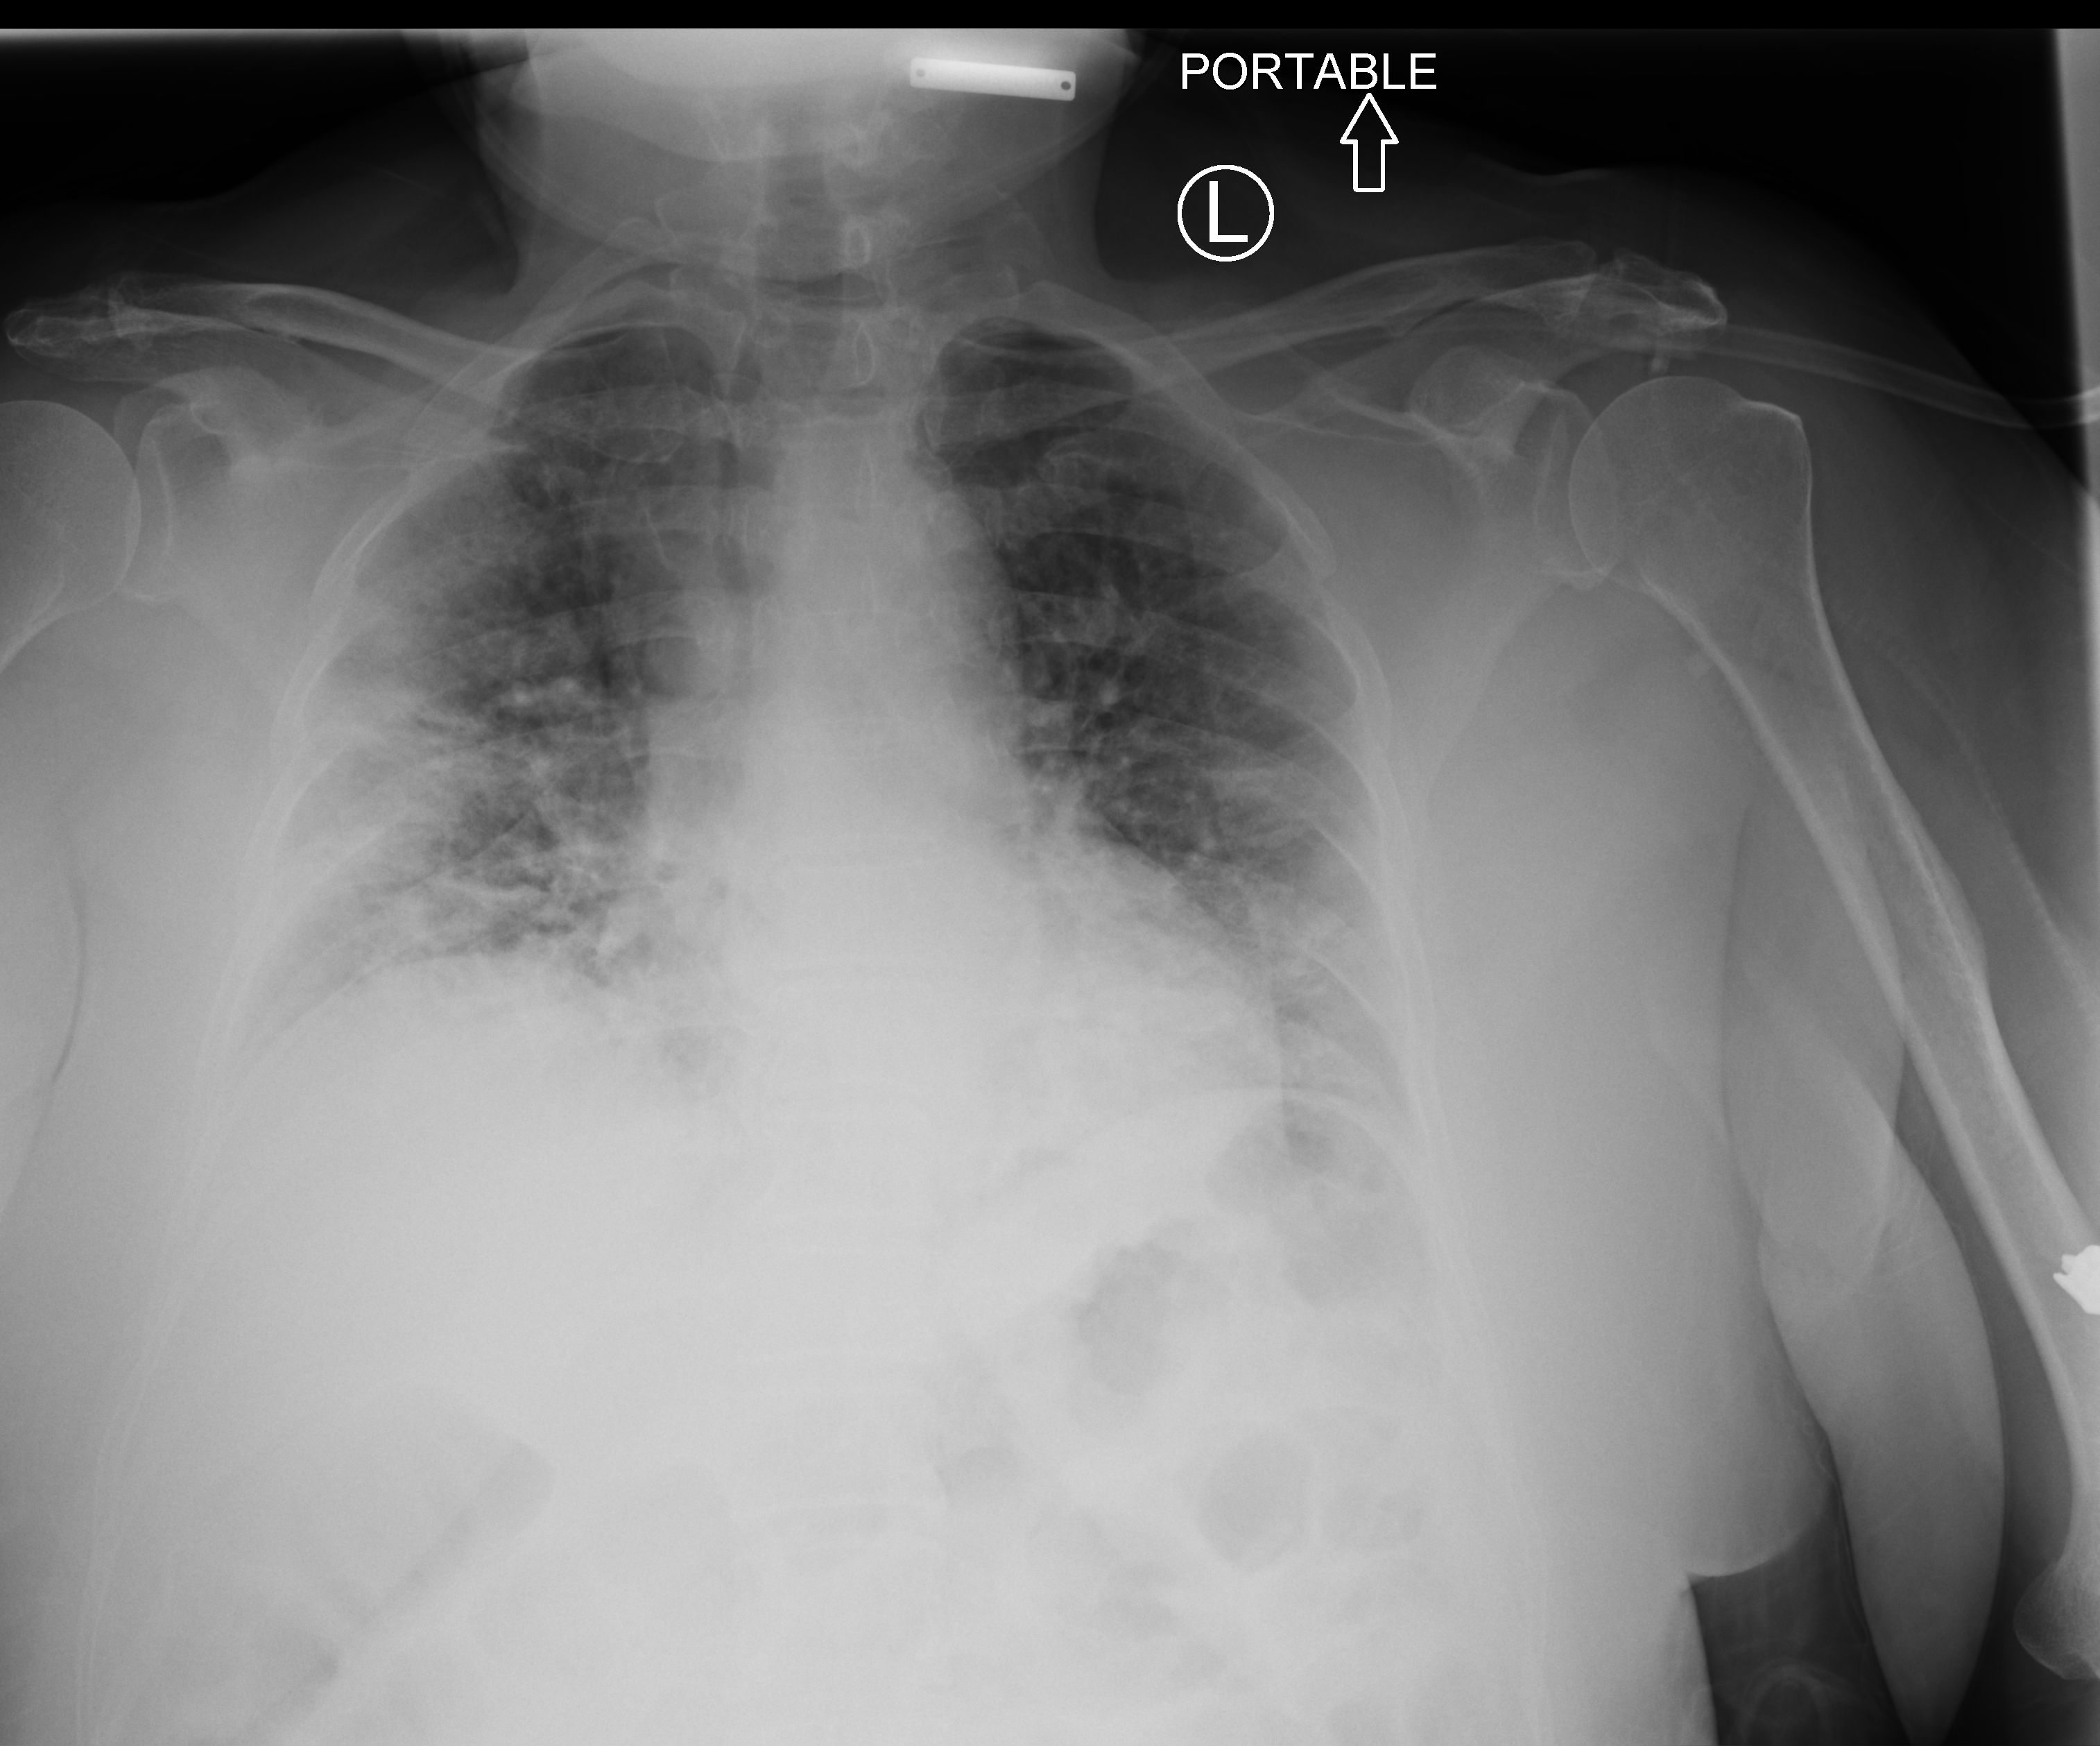
Portable chest radiograph; anteroposterior (AP) projection. Patient hospitalised with COVID-19; female, aged 60–74 years.
Hospital-stay facts (about this admission, not read from this image; timing relative to this image not recorded): admitted to intensive care during this hospital stay: no; smoking status (admission record): never.